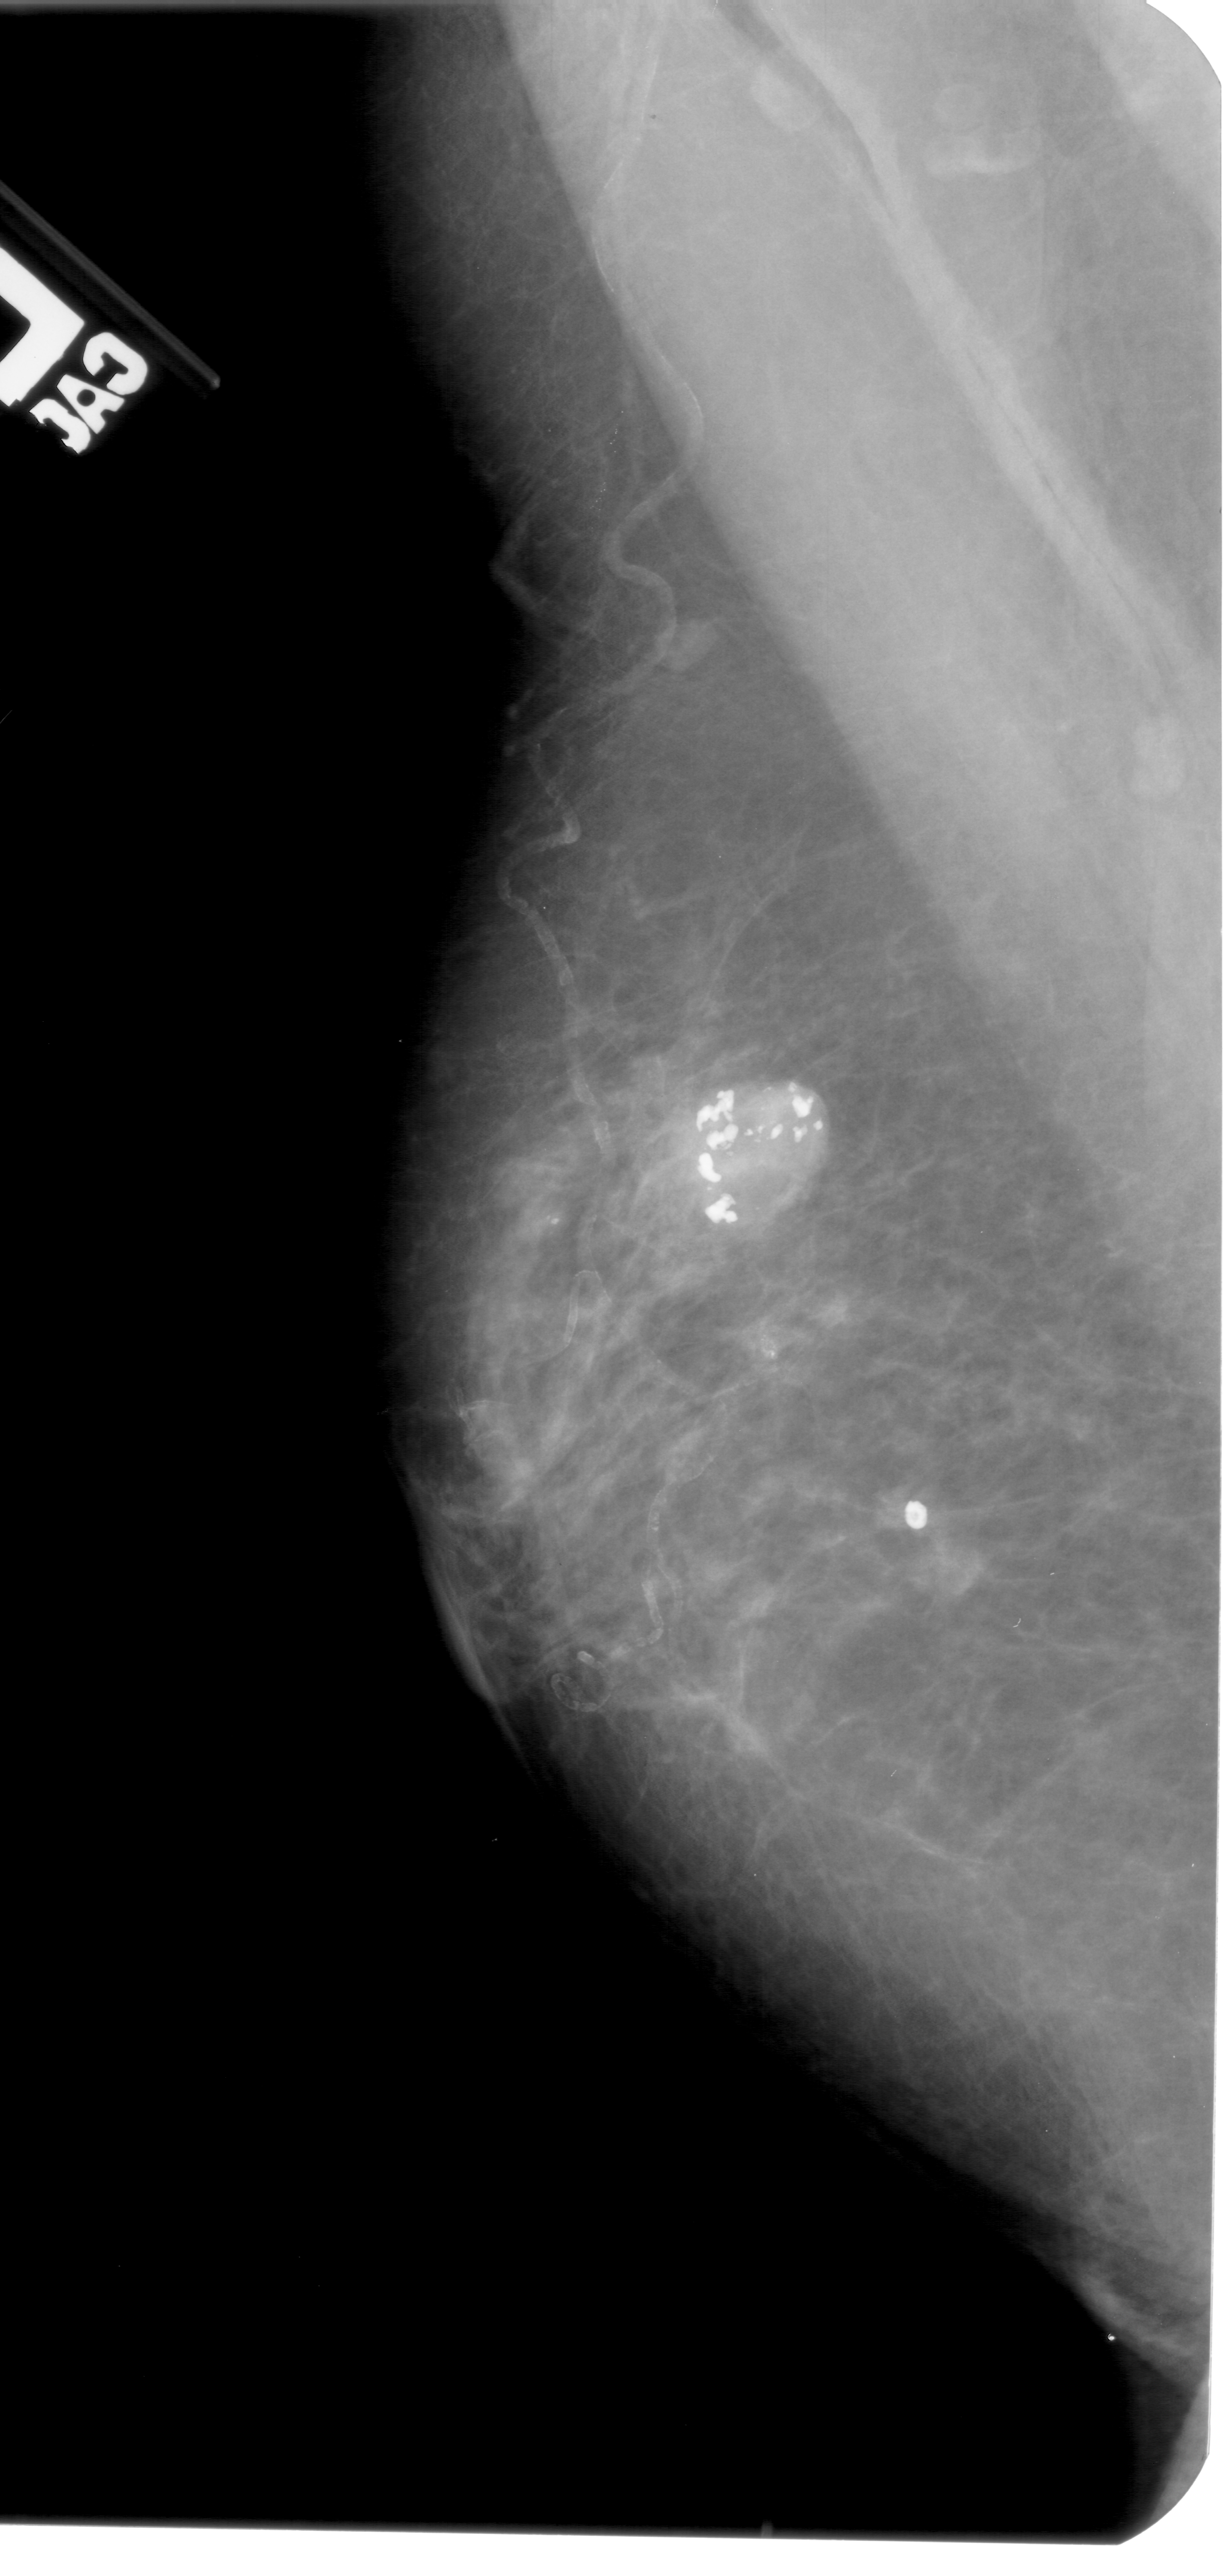
Scanned film-screen mammogram. Left breast. Mediolateral oblique (MLO) view. BI-RADS breast density category 3 (scale 1–4). 1232 × 2576 image matrix.
Expert-marked regions of interest on this film, with their recorded descriptors:
- calcifications, morphology amorphous; BI-RADS assessment category 2; subtlety rating 5 on a 1 (subtle) to 5 (obvious) scale; pathology (as recorded): benign: bounding box [x1, y1, x2, y2] px = [559, 1015, 883, 1320]